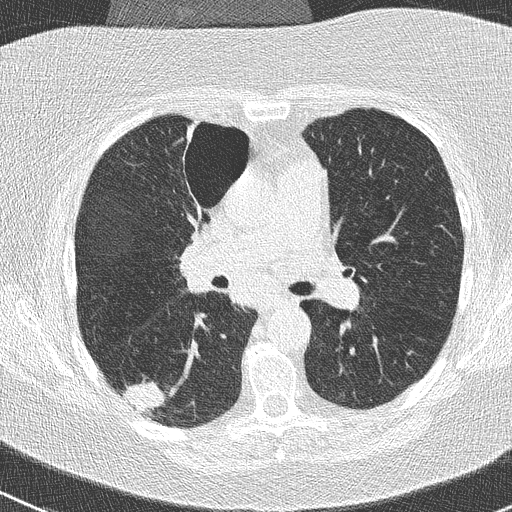
Low-dose screening chest CT, one axial slice; position 153 of 261 along the scan axis; 120 kVp; lung window (W 1500 / L -600 HU); 2 mm slice thickness; 512 × 512 image matrix, field of view 310 × 310 mm.
Outlined on this slice (outlined manually by an expert reader):
- lesion 1 (tumor, lower lobe of right lung): bounding box (x1, y1, x2, y2) in pixels: (123, 381, 166, 415)